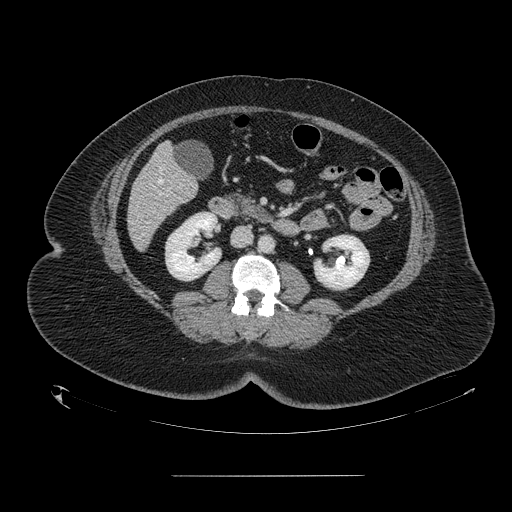
Contrast-enhanced abdominal CT, one axial slice. 120 kVp. Intravenous contrast given. Soft-tissue window (W 400 / L 40 HU). 512 × 512 image matrix, field of view 495 × 495 mm. Female patient, age 52 years. Case-level facts recorded for this patient, not image findings: diagnosis: colorectal cancer liver metastases, imaged before liver resection; multiple liver metastases: yes; largest metastasis: 3.5 cm.
Annotated regions visible in this slice (manually delineated by an expert):
- hepatic veins: bounding box [x1, y1, x2, y2] px = [158, 168, 162, 183]
- liver: [128, 145, 197, 249]